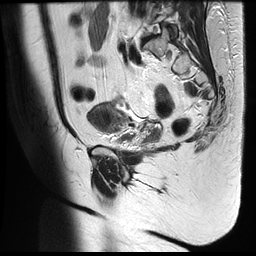
Pelvic MRI for cervical cancer, one sagittal slice. Slice 11 of 35 in the series (ordered by position). T2-weighted. 1.5 T. TE 122.8 ms, TR 4992 ms. 4 mm slice thickness. 256 × 256 image matrix, field of view 300 × 300 mm. Female patient, age 42 years.
Structures marked on this image (expert manual segmentation):
- uterus and cervix: bounding box <87,103,161,143> (left, top, right, bottom; pixels)